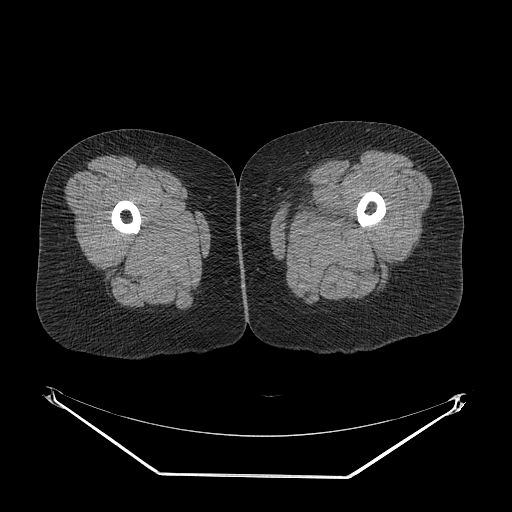
CT of an extremity soft-tissue mass (from a PET/CT study), one axial slice; slice 9 of 267 in the series (ordered by position); reconstruction kernel STANDARD; soft-tissue window (W 400 / L 40 HU); 512 × 512 image matrix, field of view 500 × 500 mm. Female patient. From the clinical record (not read from this slice): histological type: myxofibrosarcoma; grade: intermediate; site of the primary tumour: left thigh.
Annotated regions visible in this slice (expert contour drawn on MRI and transferred to this co-registered scan by the dataset authors):
- gross tumour volume including surrounding oedema: bounding box <281,198,350,238> (left, top, right, bottom; pixels)